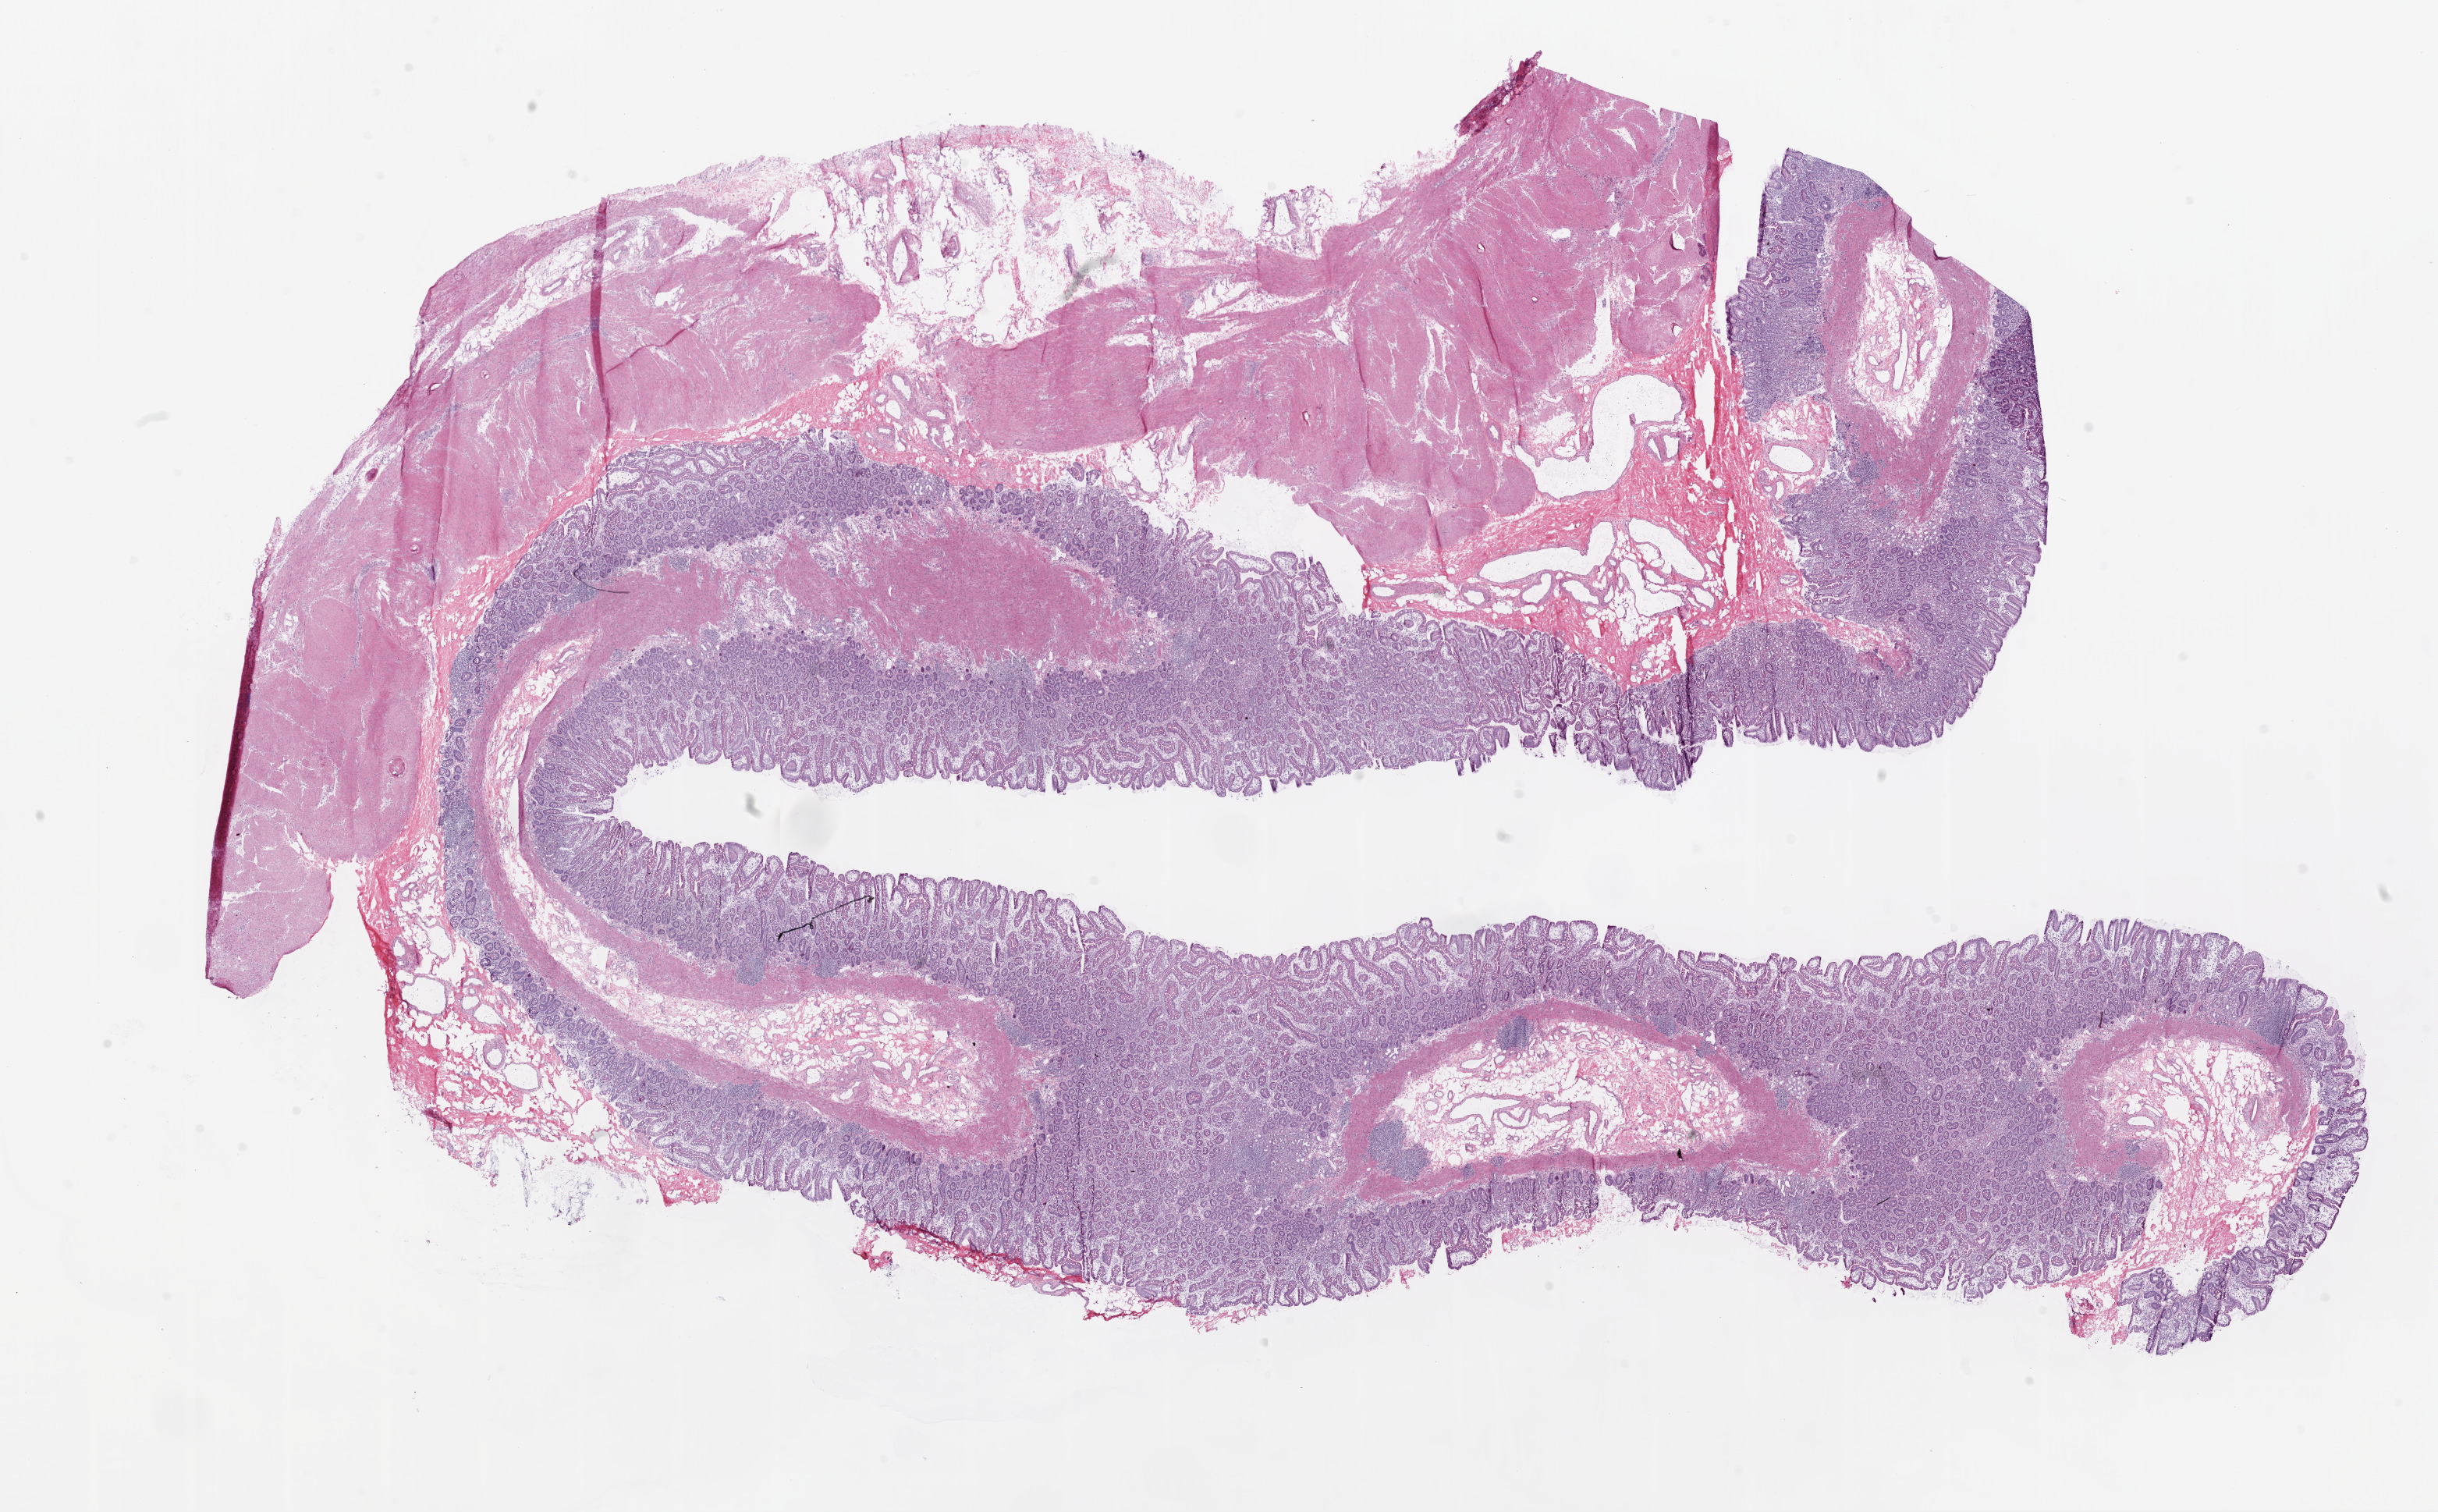
Whole-slide histology image, H&E-stained — low-resolution overview of the scanned area, about 25.1 x 15.6 mm (from a 20x scan). Frozen section from the top of the tissue portion. Stomach, solid tissue normal (non-tumour tissue) sample. Male, age 75 years at initial diagnosis.
• this section: solid tissue normal sample (biorepository sample class)
• patient diagnosis: Adenocarcinoma, NOS (cardia, NOS)